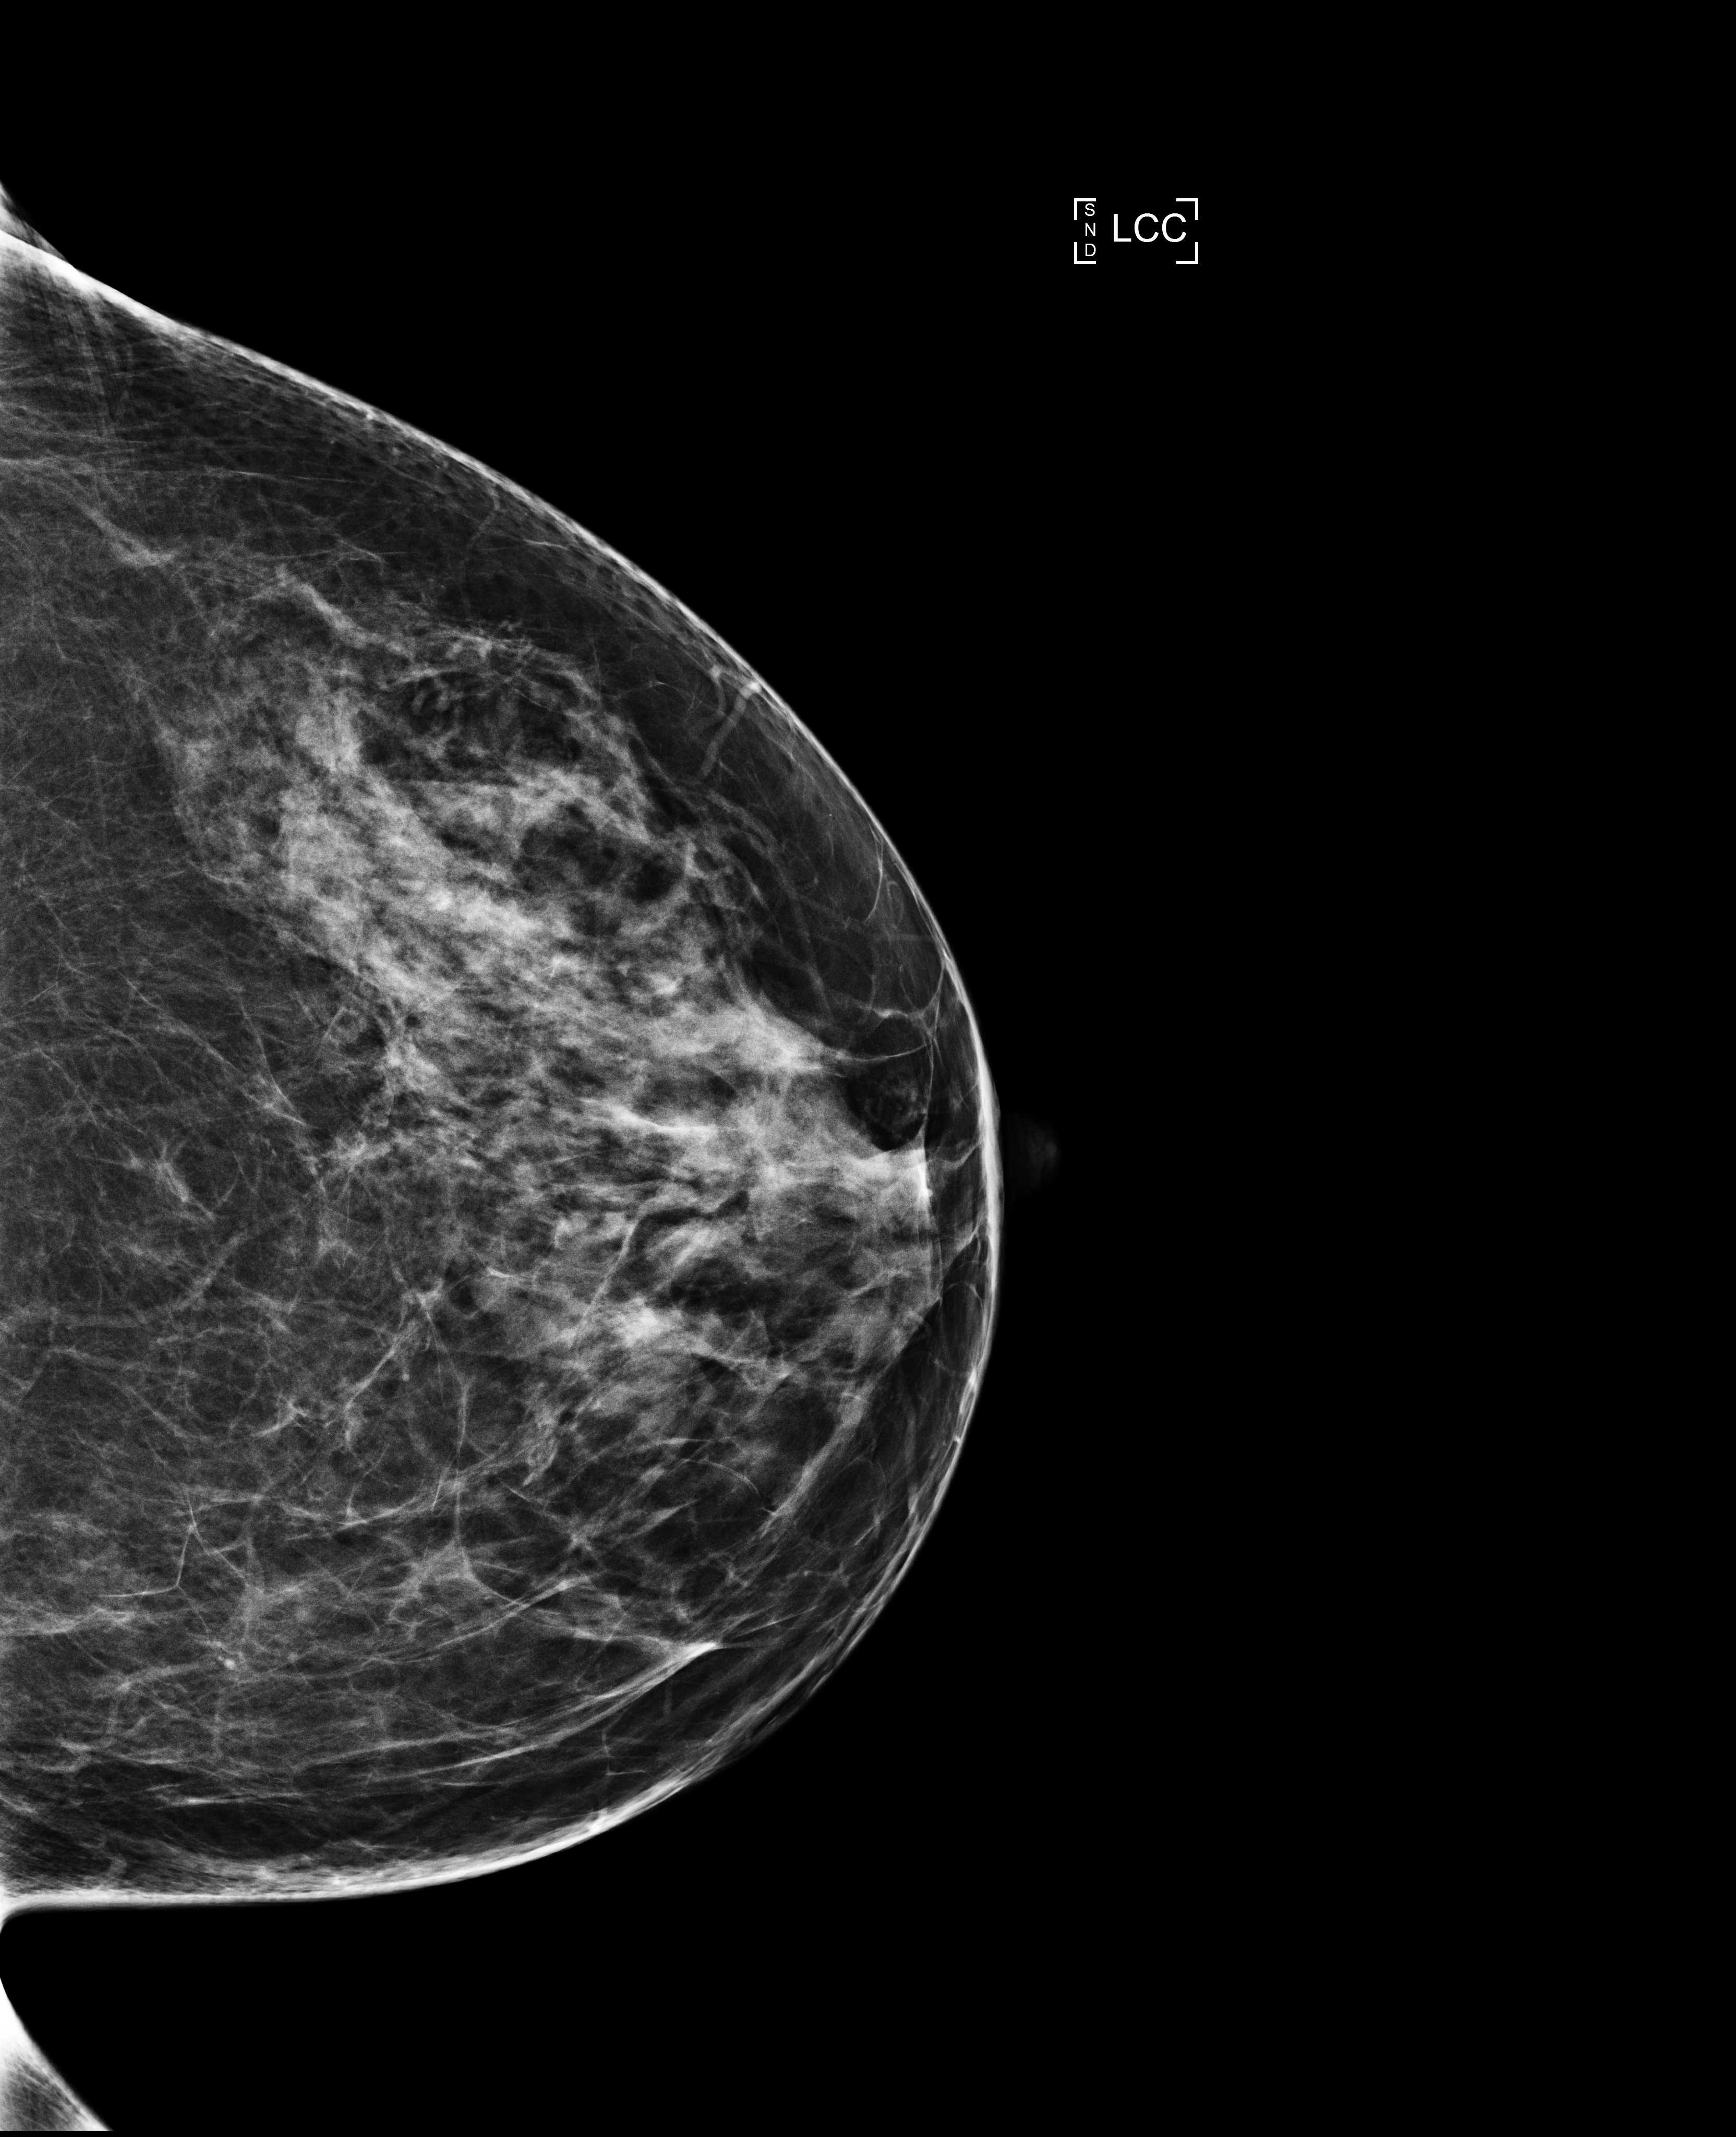
Annual screening mammography examination. Patient: female, 54 years.
Image type: full-field digital mammogram. Breast: left. Projection: CC view.